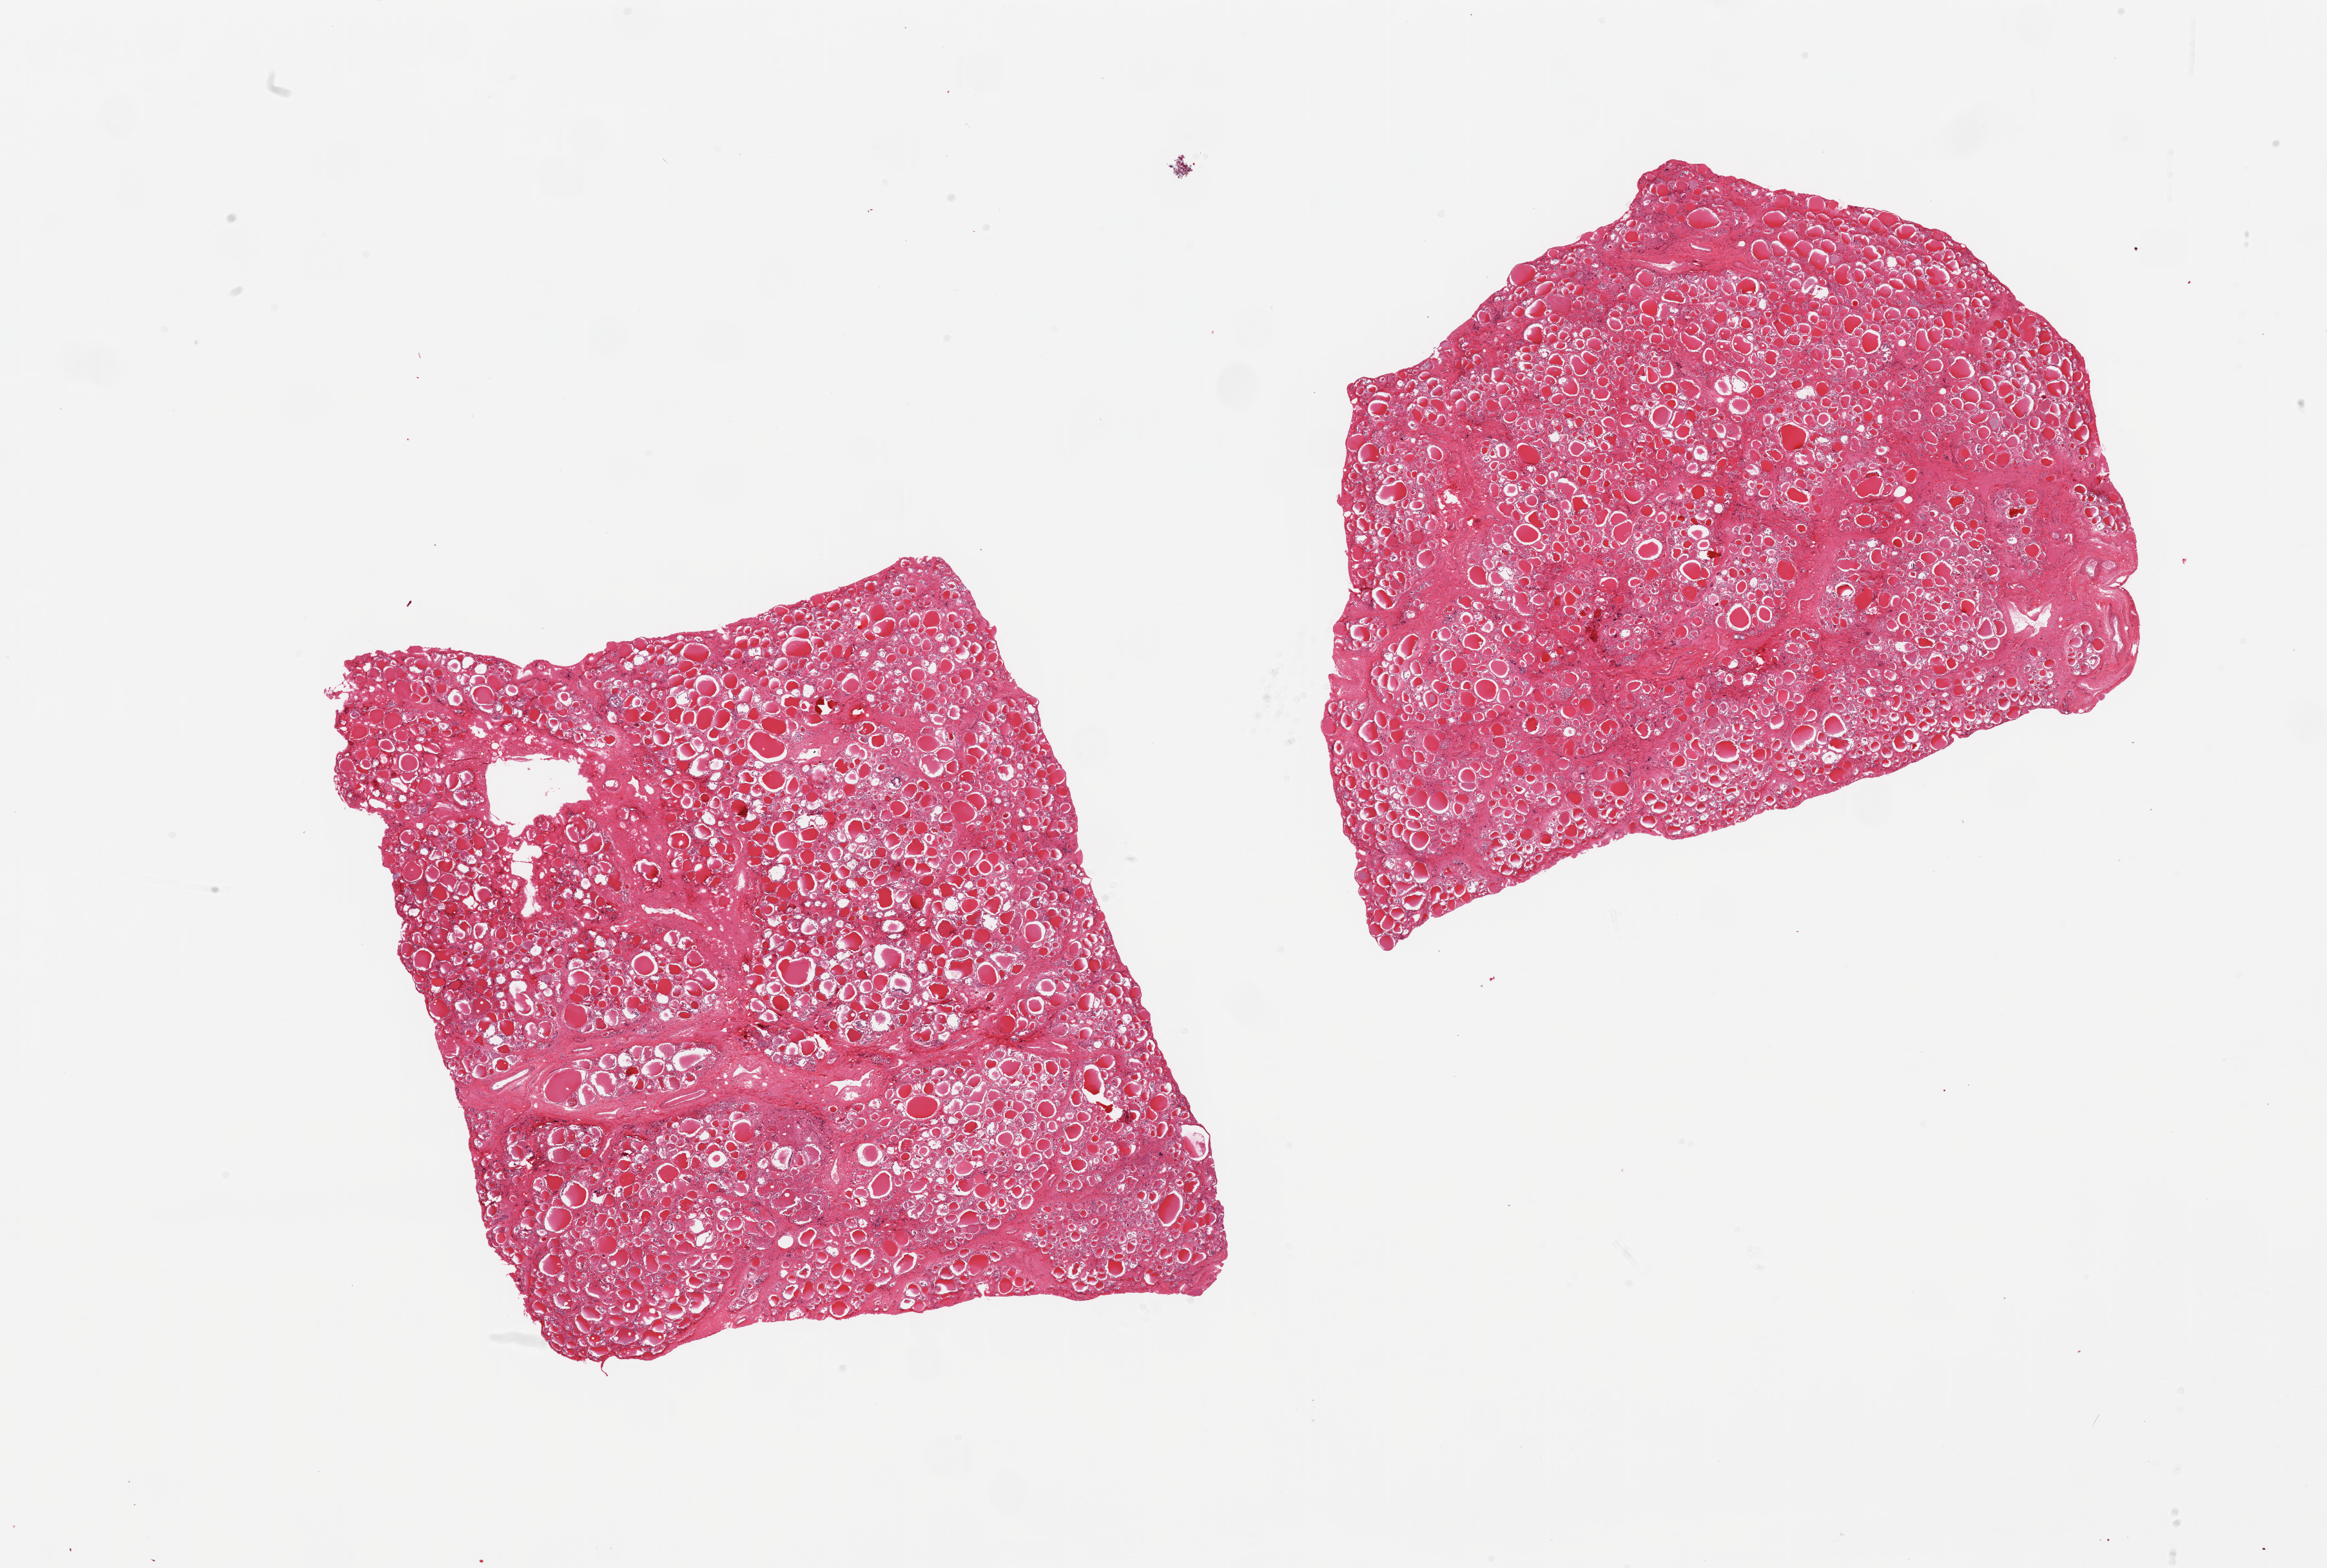
Haematoxylin and eosin whole-slide image, low-resolution overview of the scanned area, about 28.5 x 19.2 mm (slide scanned at 20x), PAXgene-fixed, paraffin-embedded tissue, target tissue: thyroid, donor tissue sample. Donor sex: male.
Review note (as recorded): 2 pieces.